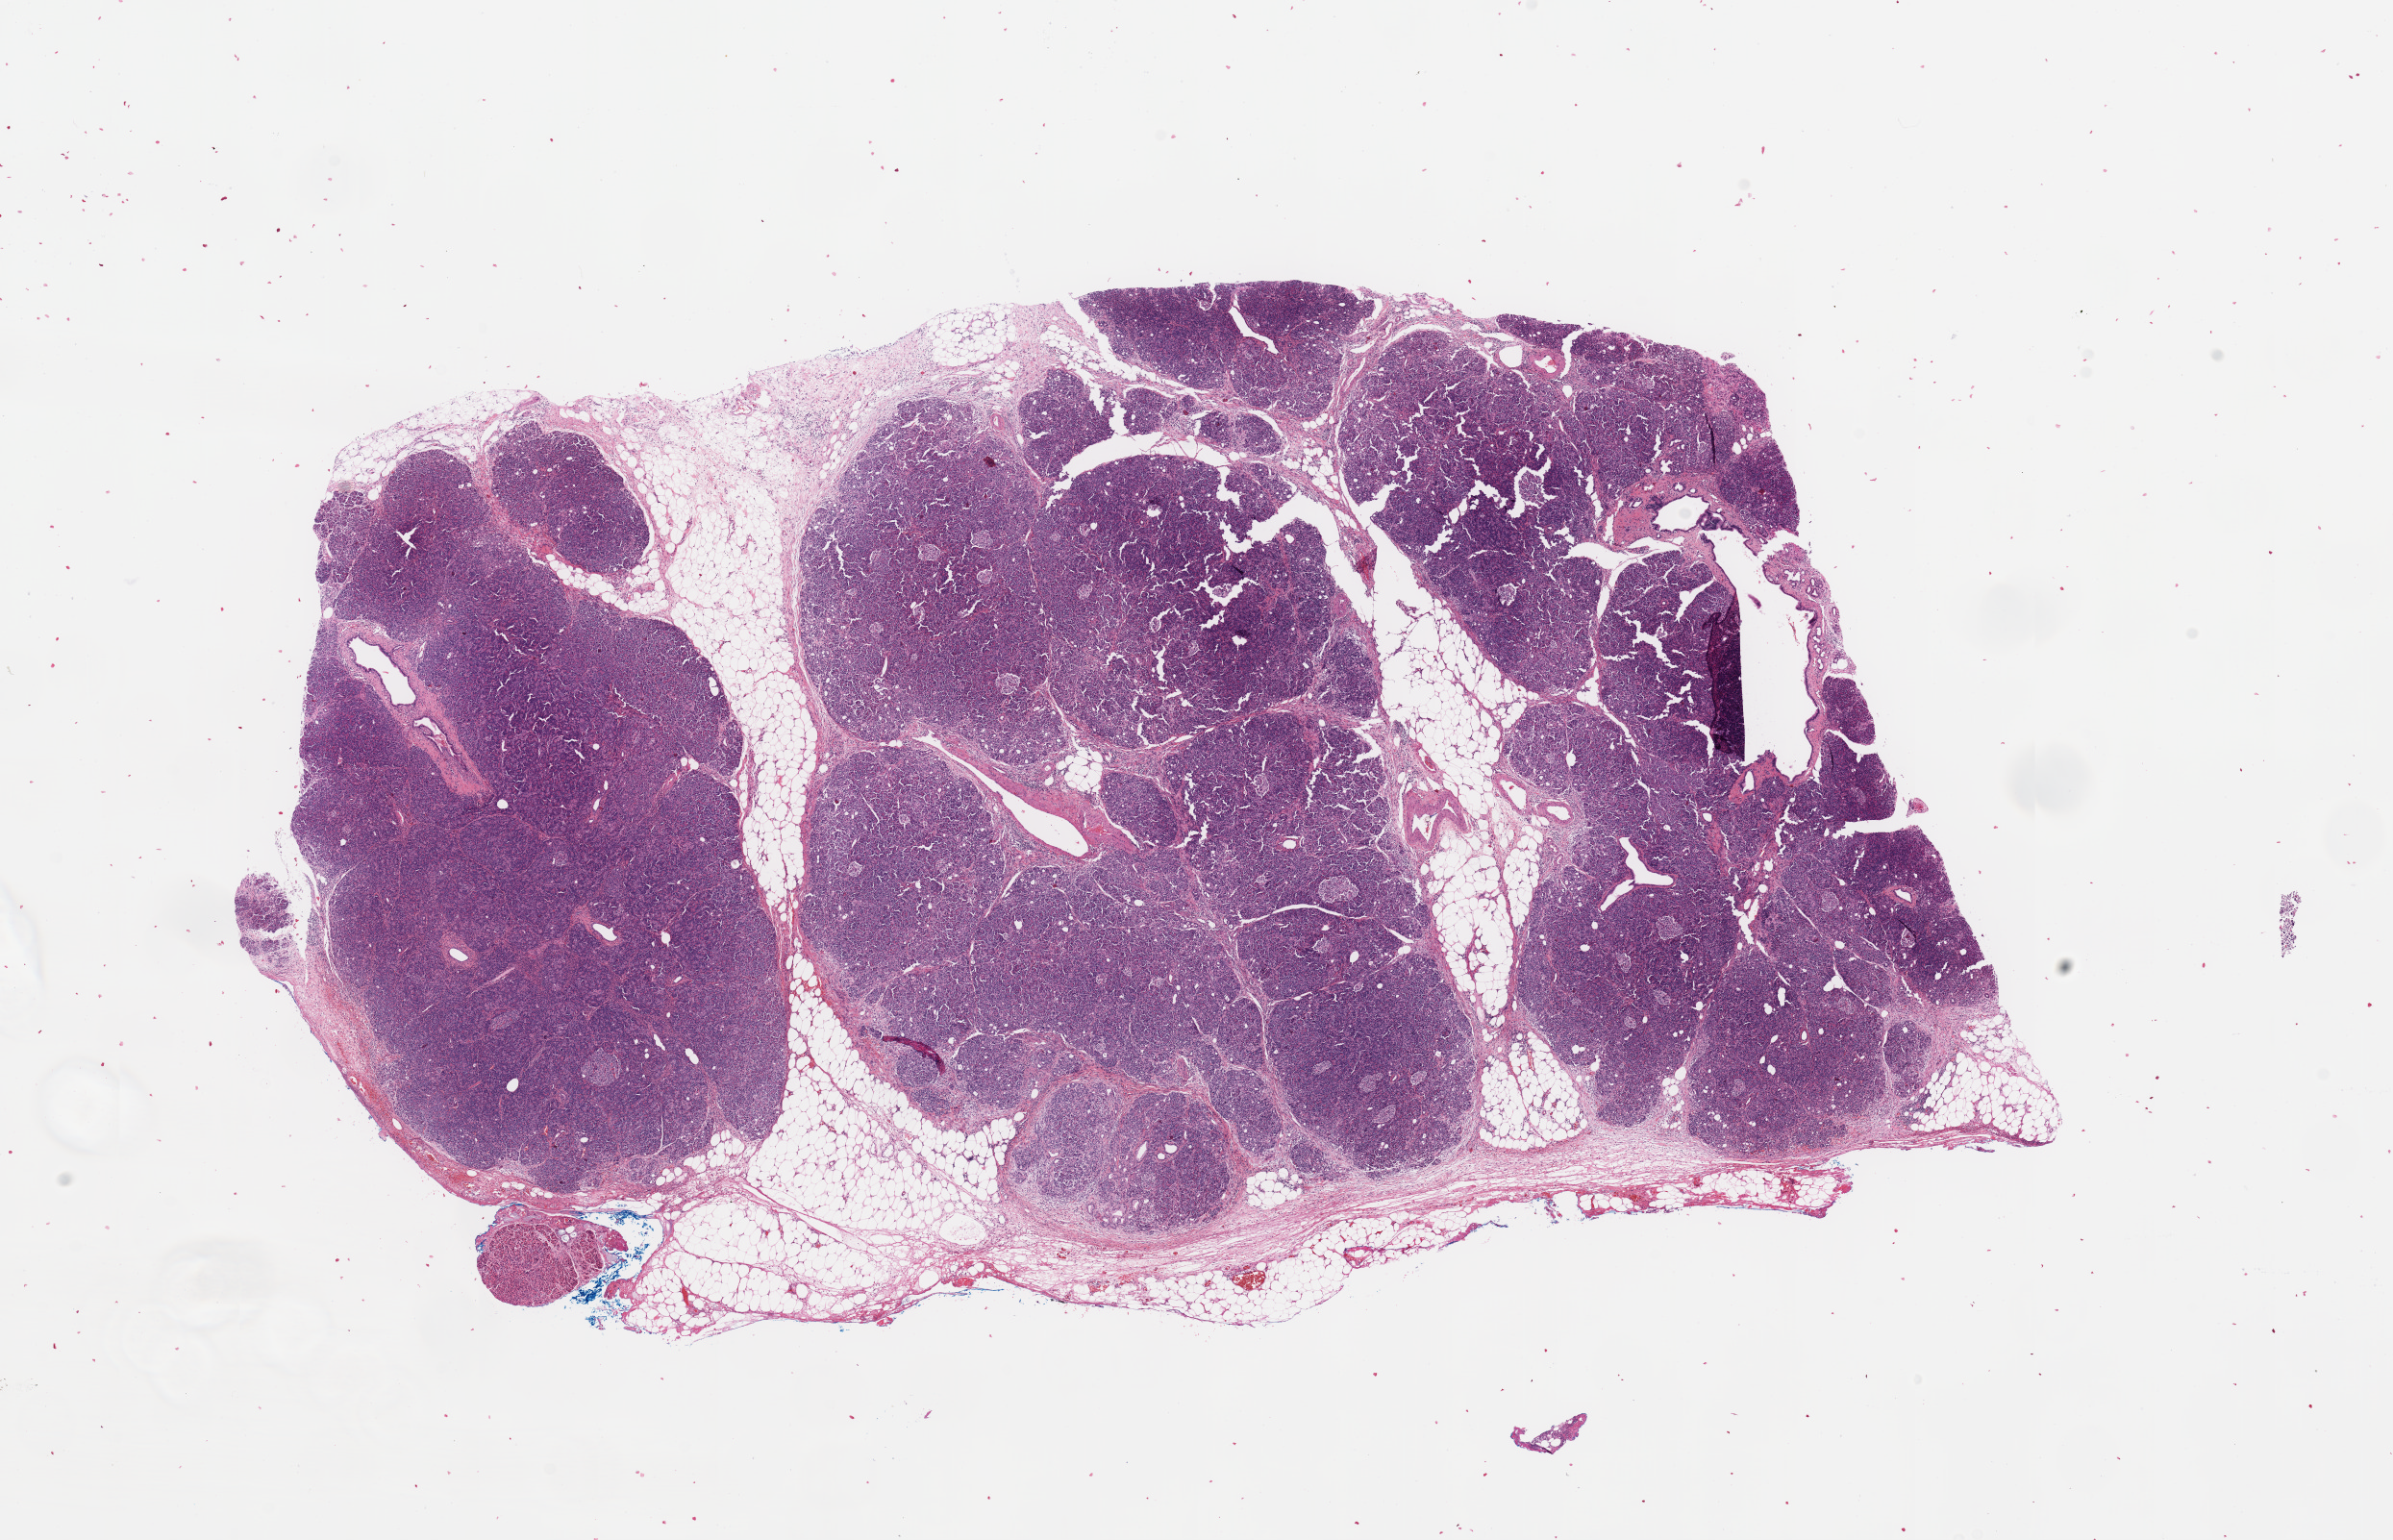
Digitized Hematoxylin and eosin (H&E) stained tissue section (whole slide) — a low-resolution overview of the entire scanned area, about 19.7 x 12.7 mm (acquisition: 20x scan). Normal (non-tumour) tissue sample, sampled site: pancreas. 68-year-old female patient.
* this section: normal (non-tumour) tissue from the same patient
* patient diagnosis: Infiltrating duct carcinoma, NOS